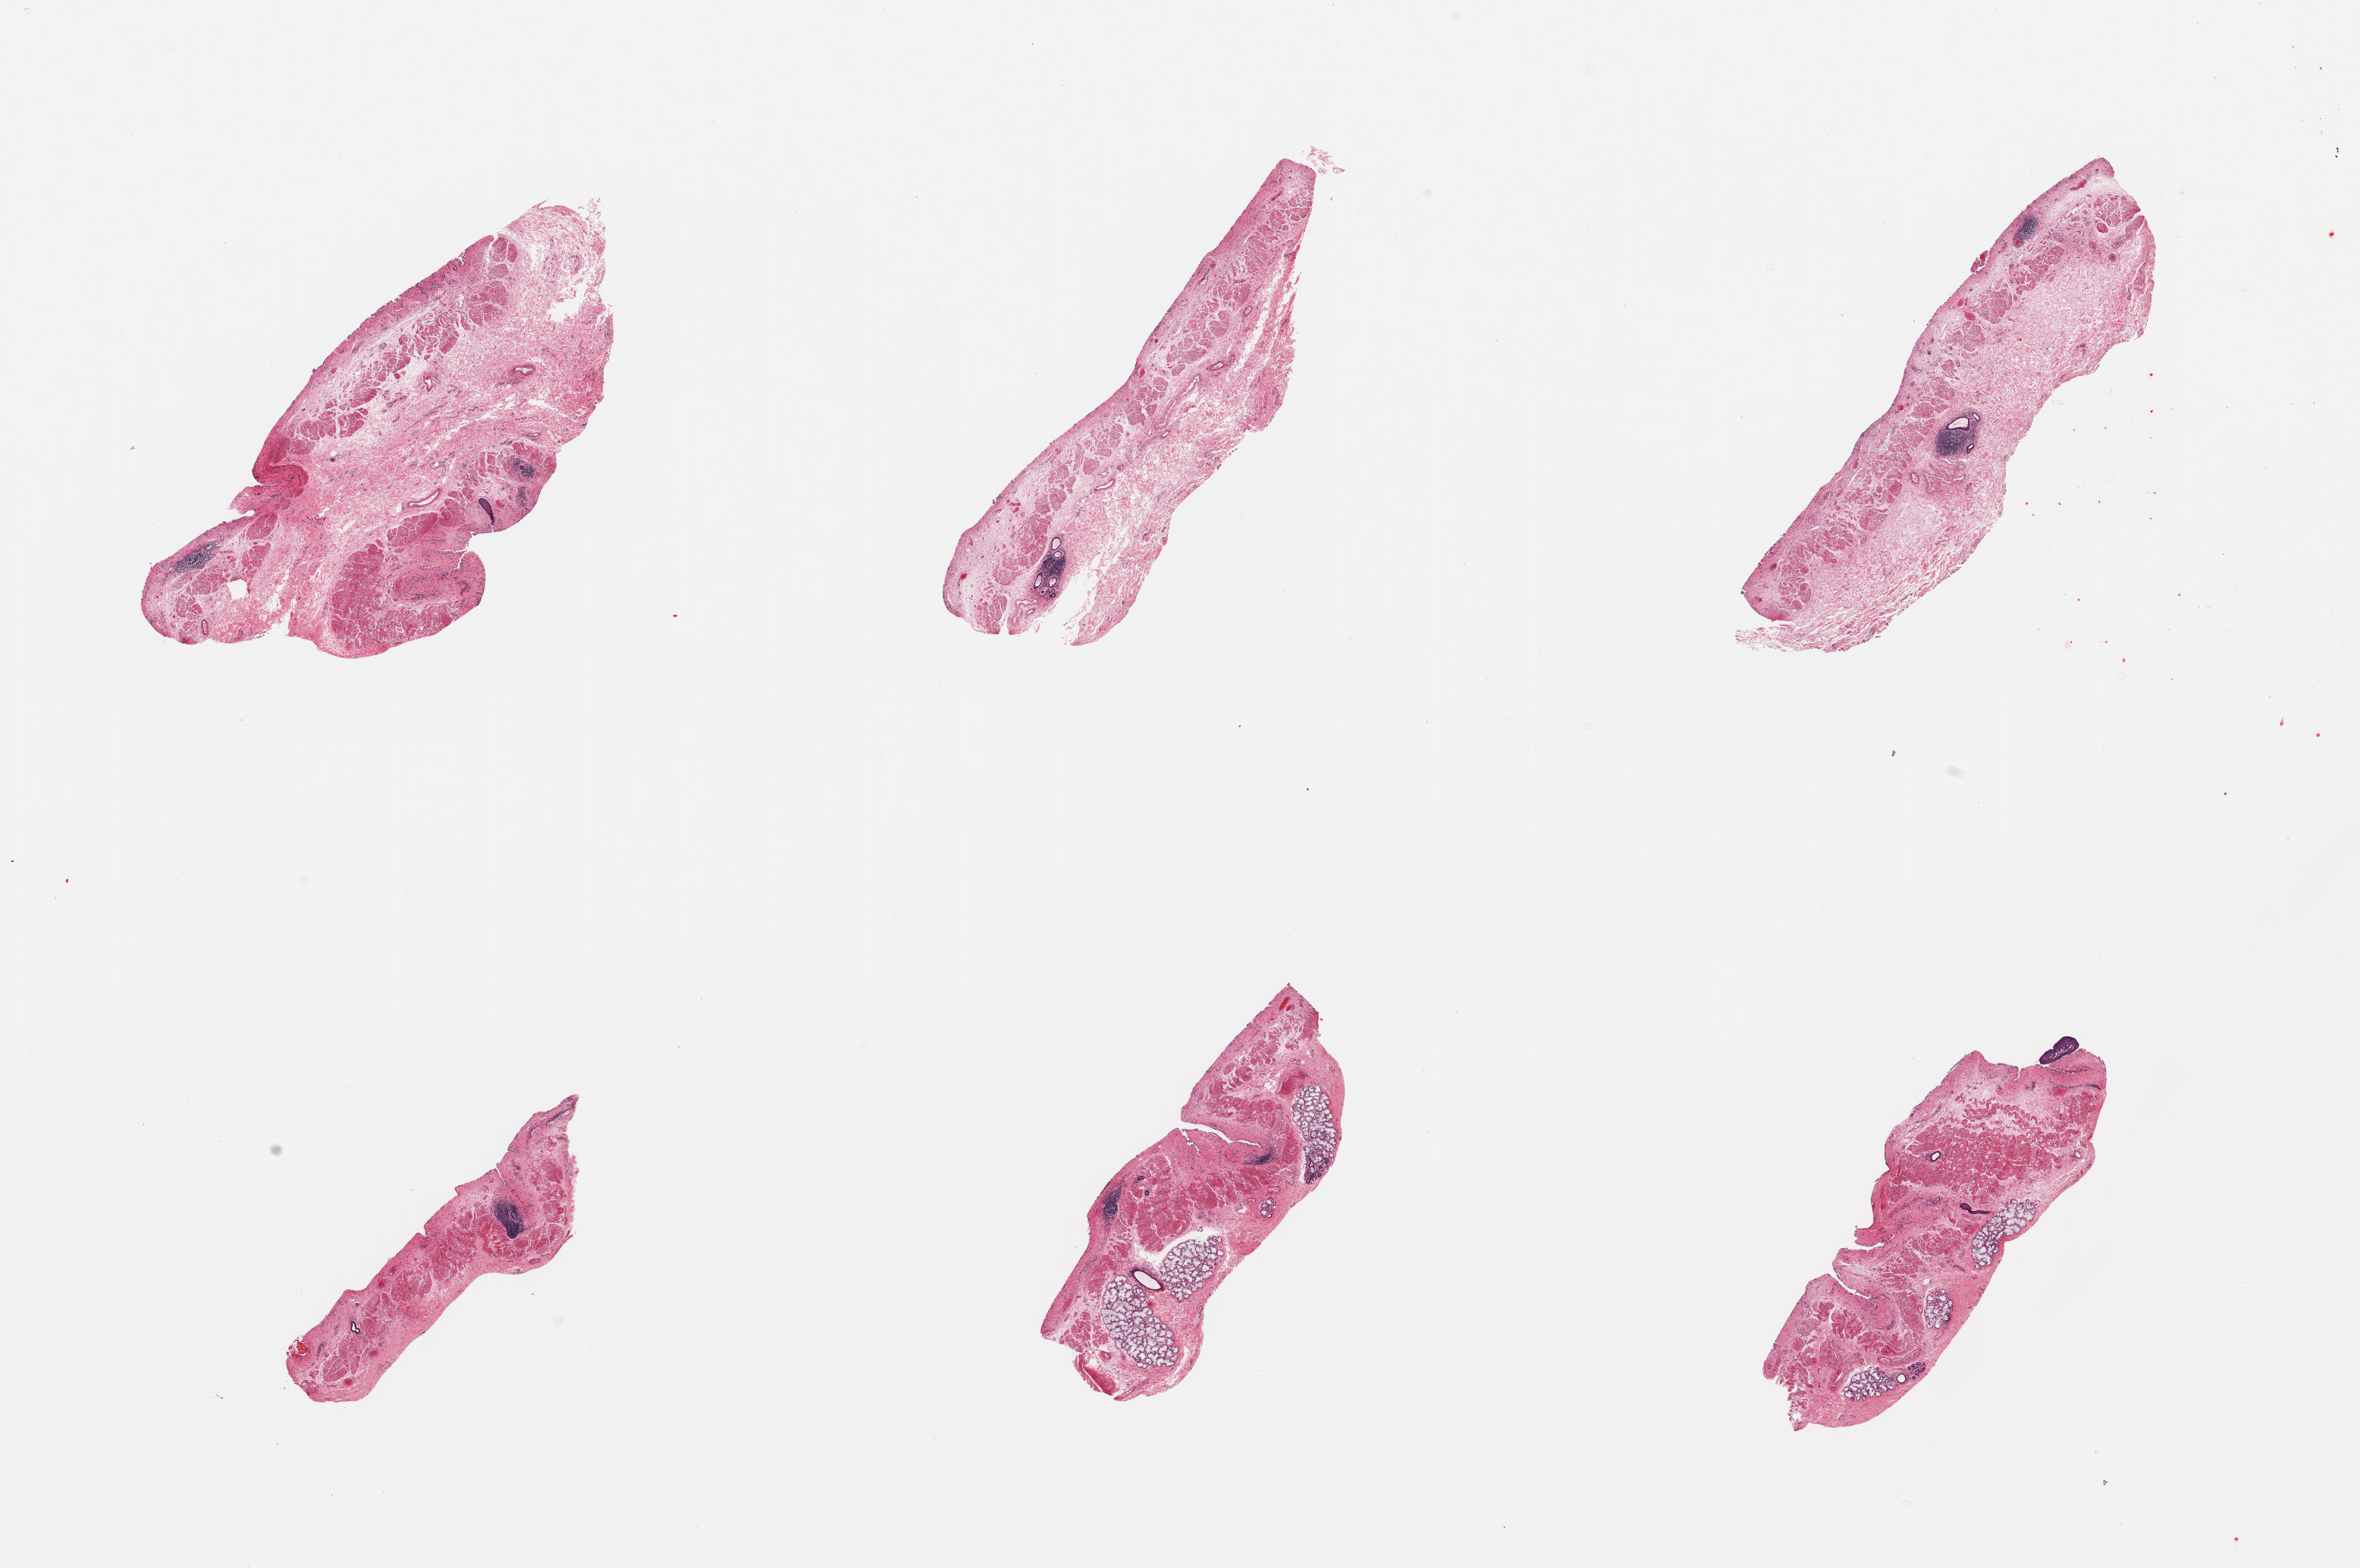
Digitized haematoxylin and eosin-stained section — shown as a low-resolution overview of the whole scanned area (about 24.6 x 16.4 mm). PAXgene-fixed paraffin-embedded (PFPE) section. Sampled site (target tissue): esophageal mucous membrane. Donor tissue sample. Male donor.
Review note (as recorded): 6 pieces, mucosa largely sloughed; hemorrhagic stroma; Submucosal mucus glands intact.